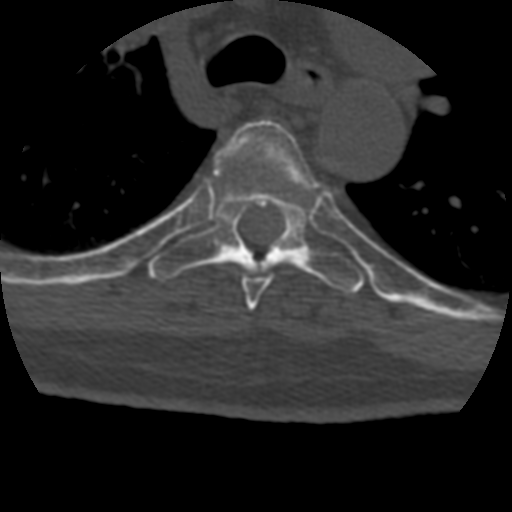
CT including the spine, one axial slice; slice 309 of 399 in the series (ordered by position); 120 kVp; bone window (W 1800 / L 400 HU); 1.25 mm slice thickness; 512 × 512 image matrix, field of view 160 × 160 mm. Patient age 69 years. From the clinical record (not read from this slice): primary cancer: prostate.
Annotated regions visible in this slice (semi-automatic segmentation, software-assisted and operator-edited):
- T5 vertebra: bounding box [x1, y1, x2, y2] px = [221, 119, 320, 311]
- T6 vertebra: [148, 158, 365, 294]